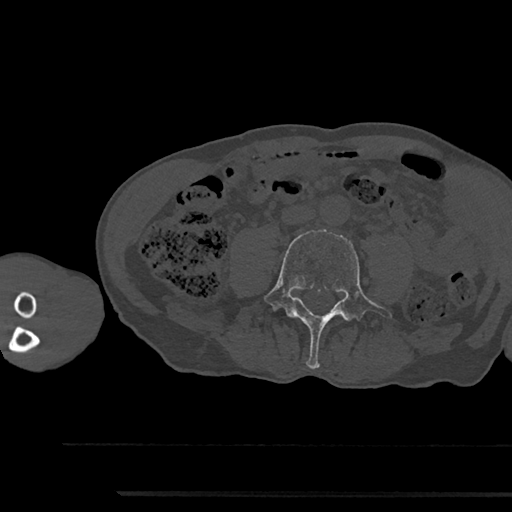
CT including the spine, one axial slice; bone window (W 1800 / L 400 HU); 512 × 512 image matrix, field of view 367 × 367 mm. Patient: male, 79 years. From the clinical record (not read from this slice): primary cancer: prostate.
Outlined on this slice (semi-automatic segmentation, software-assisted and operator-edited):
- L4 vertebra: bounding box [x1, y1, x2, y2] px = [263, 230, 392, 369]